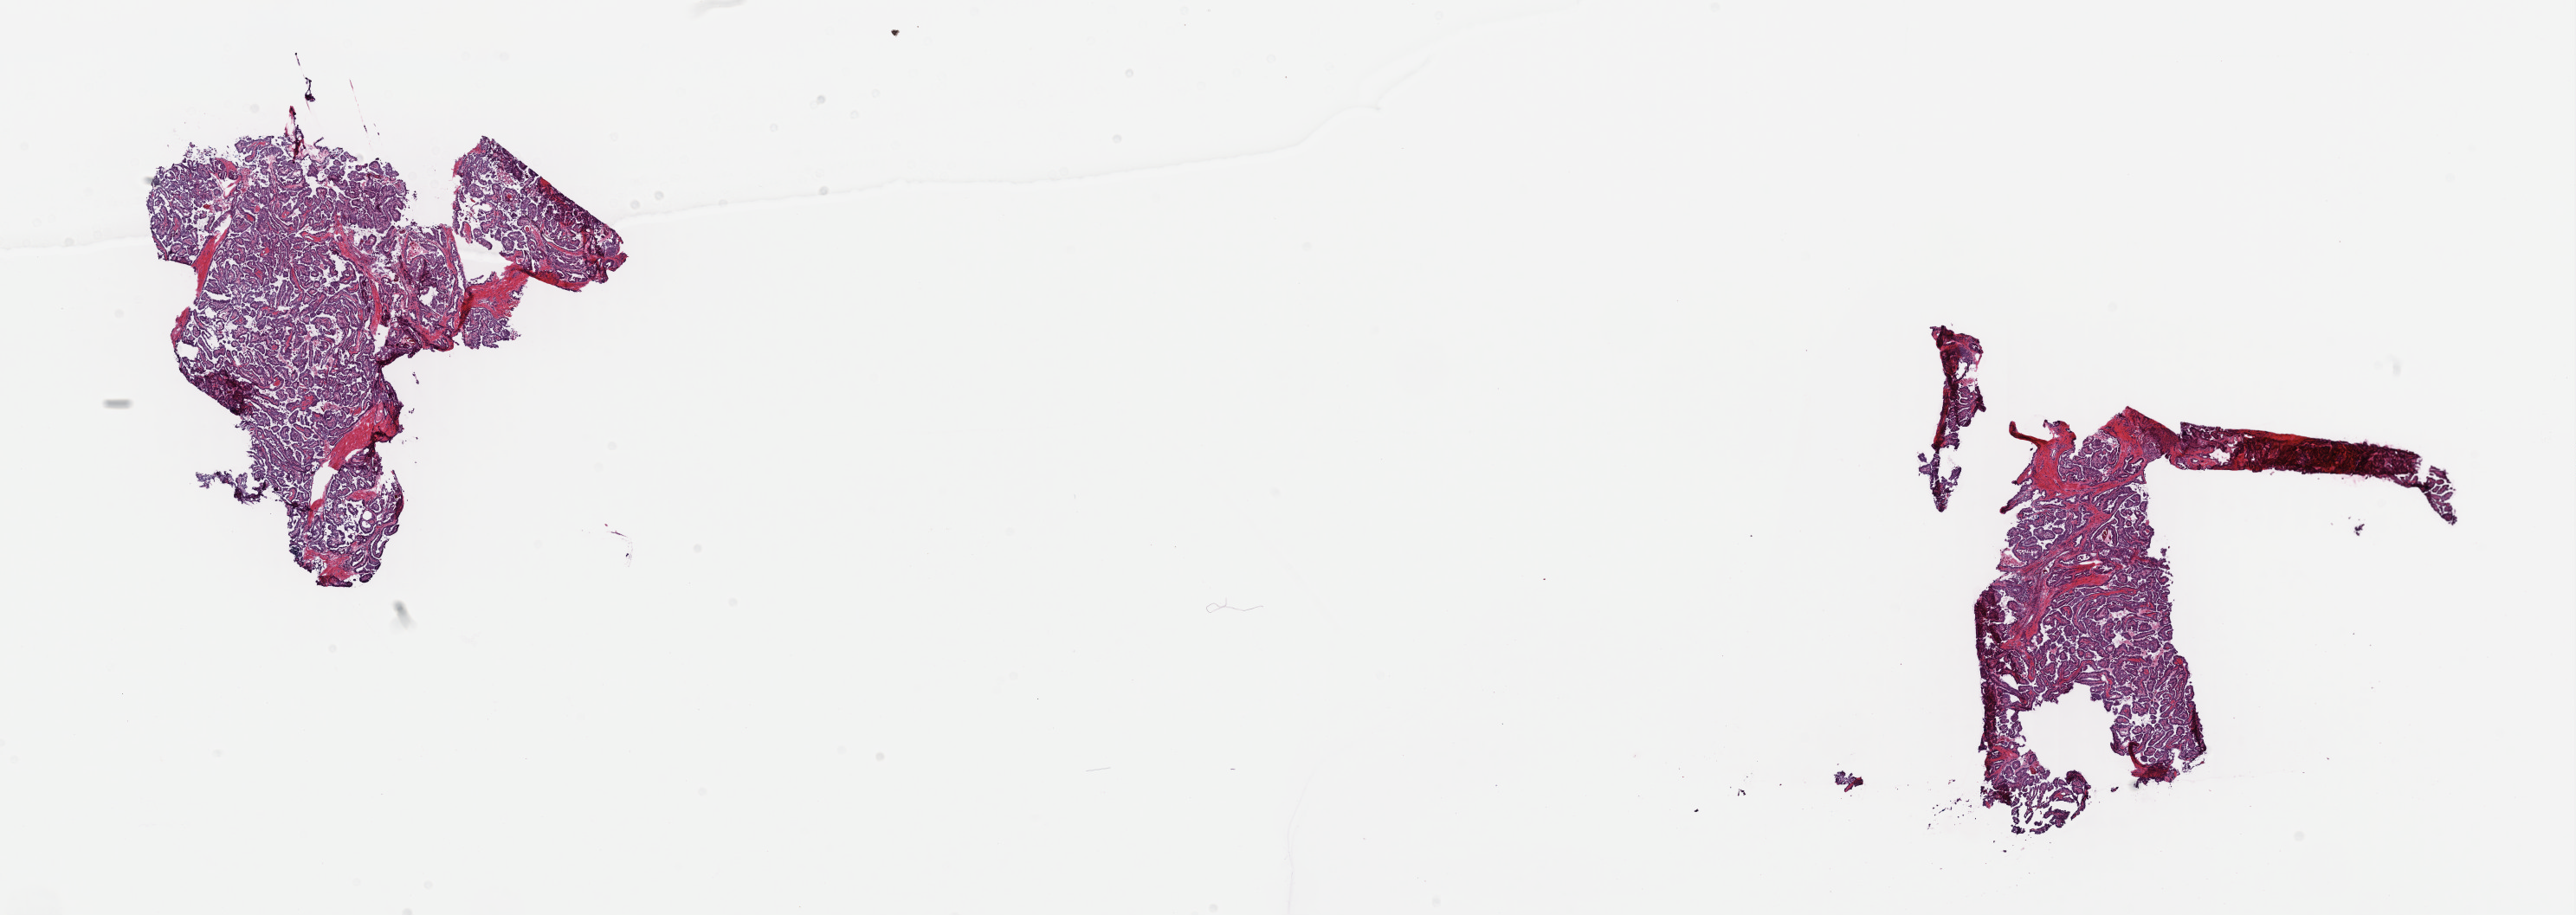
Hematoxylin and eosin (H&E) stained whole-slide image, shown as a low-resolution overview of the whole scanned area (about 23.5 x 8.3 mm); frozen section; thyroid, primary tumour sample. Male patient; age at initial diagnosis 69 years. Composition of this section per pathologist review: tumour cells 85%, tumour nuclei 85%, normal cells 0%, stromal cells 15%, necrosis 0%. Inflammatory infiltration, as recorded: lymphocyte infiltration 1%, monocyte infiltration 1%, neutrophil infiltration 0%.
Histologic diagnosis: Papillary carcinoma, columnar cell. AJCC pathologic stage: III (7th edition). TNM: T3 N0 M0. Laterality: bilateral.